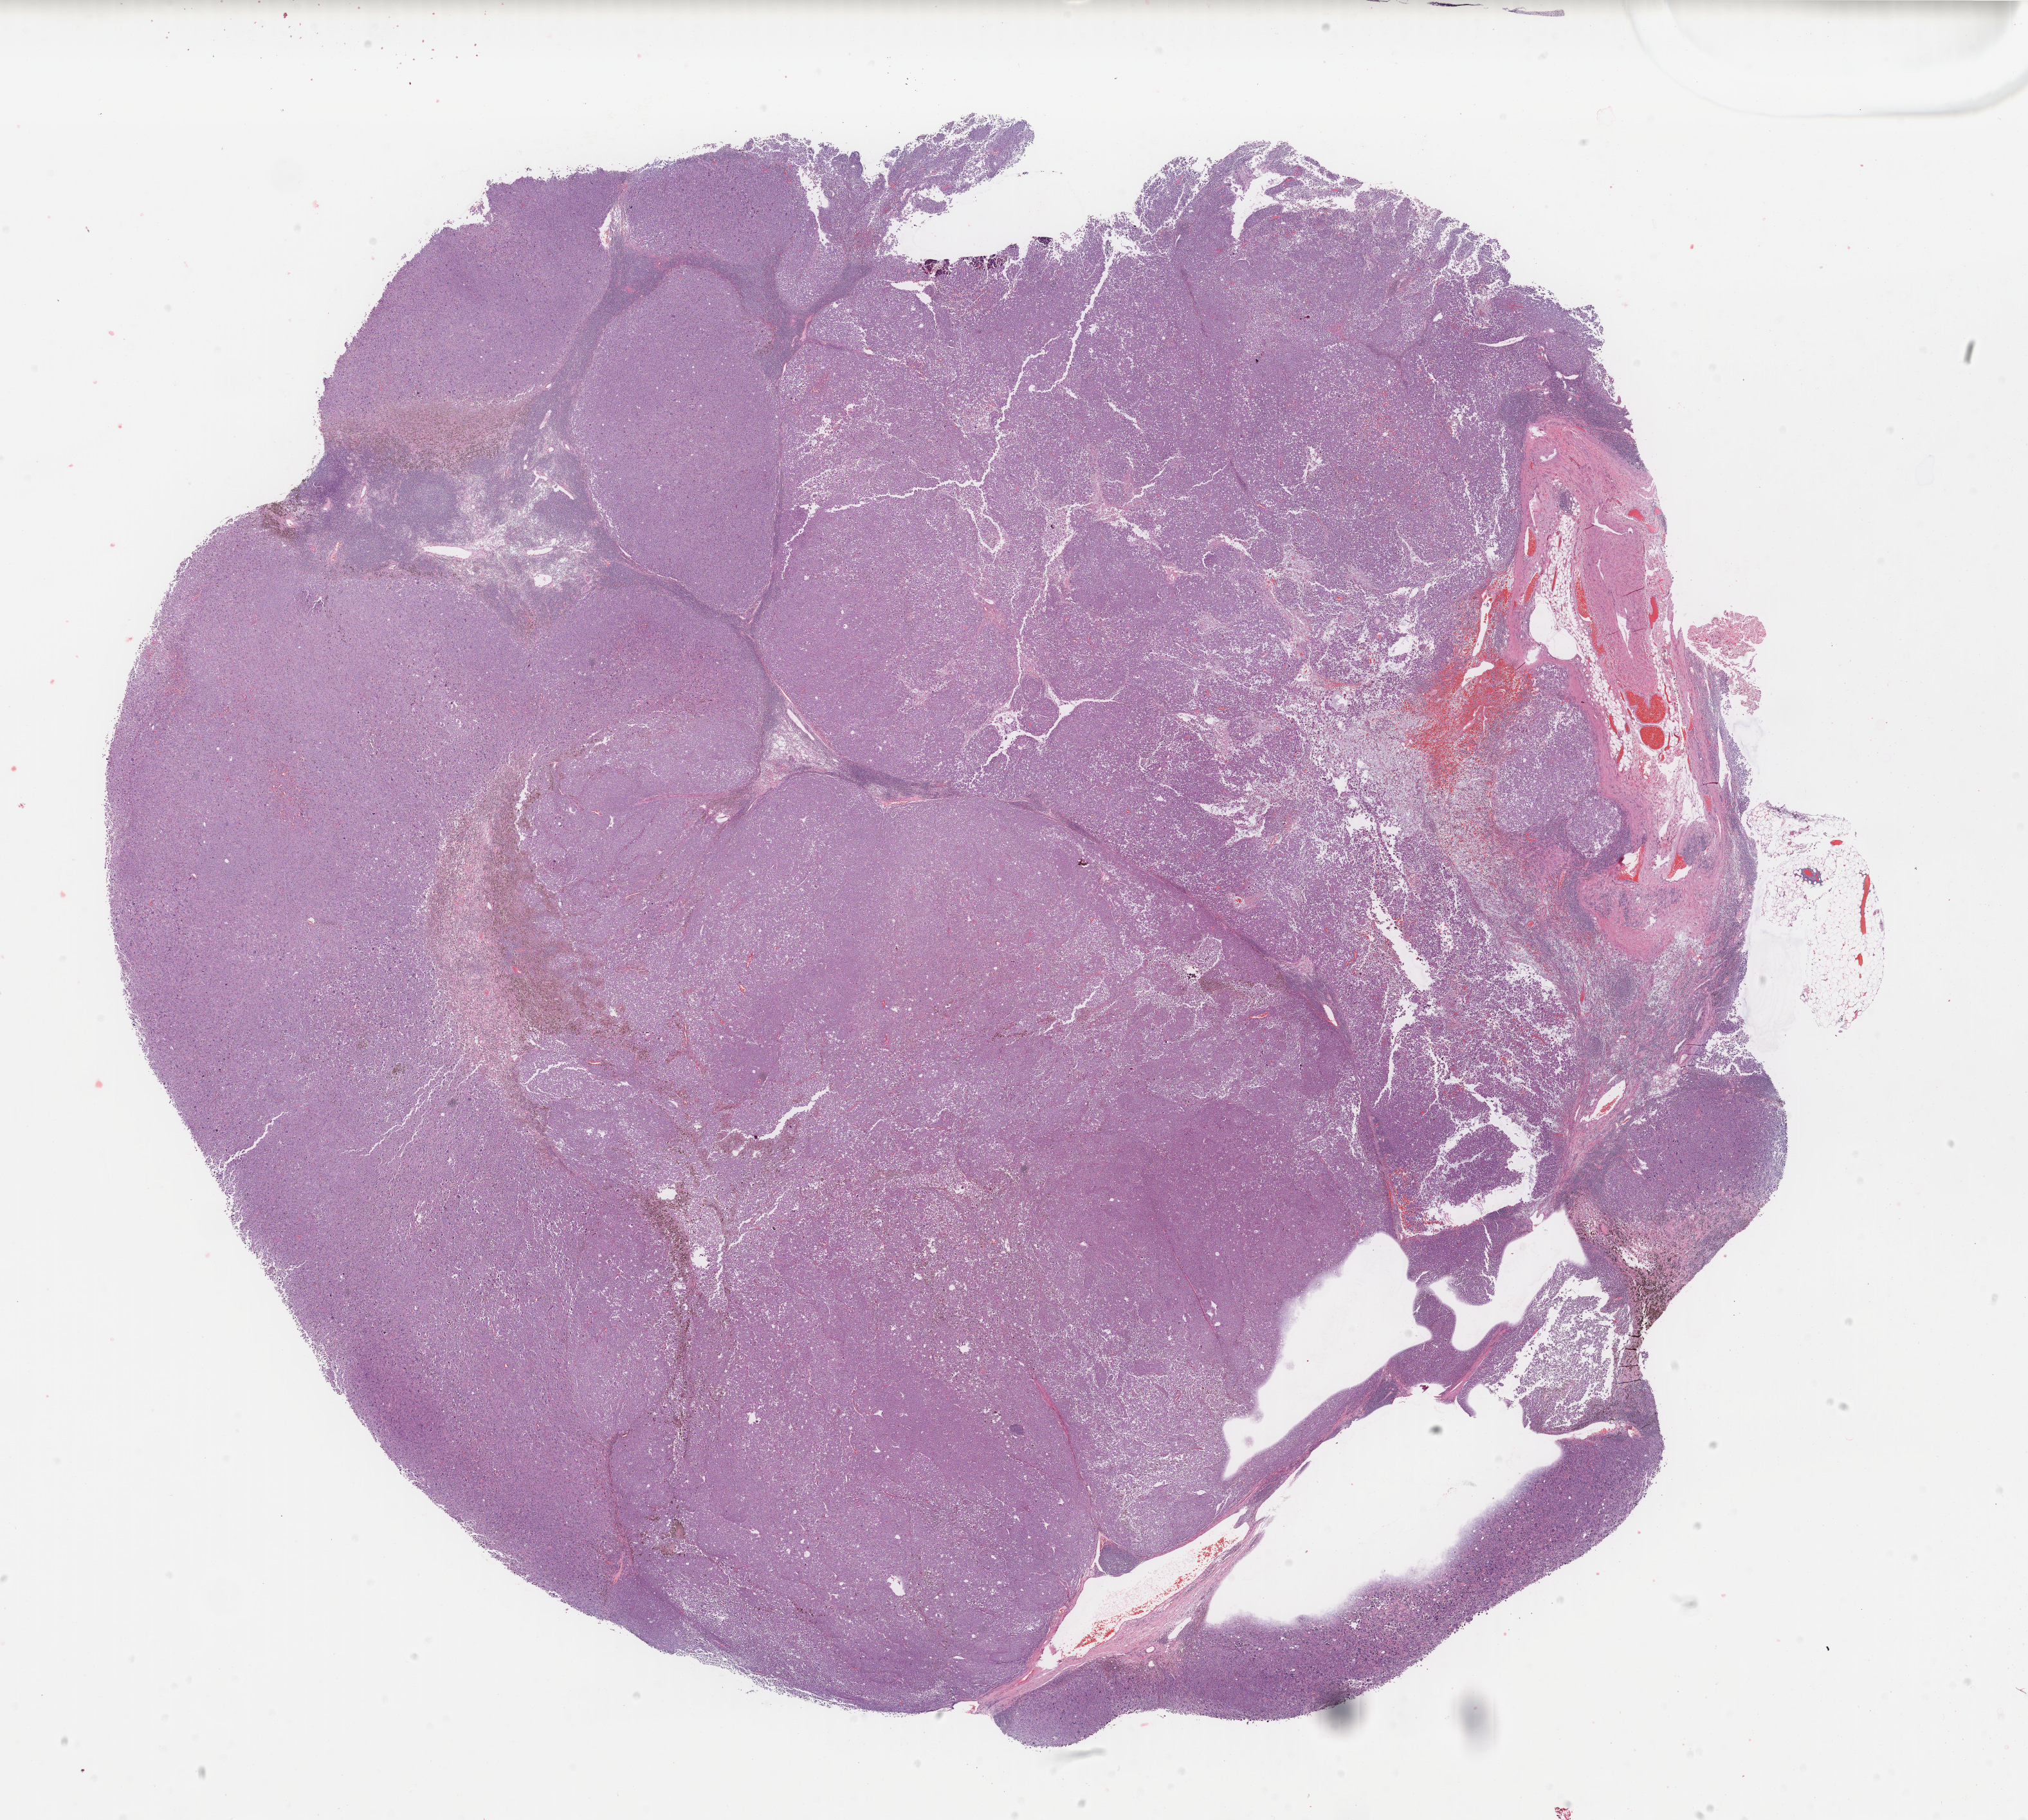
Hematoxylin and eosin (H&E) stained whole-slide image, whole scanned area (about 25.0 x 22.5 mm) shown as a low-resolution overview, FFPE section, metastatic tumour sample. Female patient; age at initial diagnosis 83 years.
This section: metastatic tumour tissue. Patient diagnosis: Malignant melanoma, NOS.